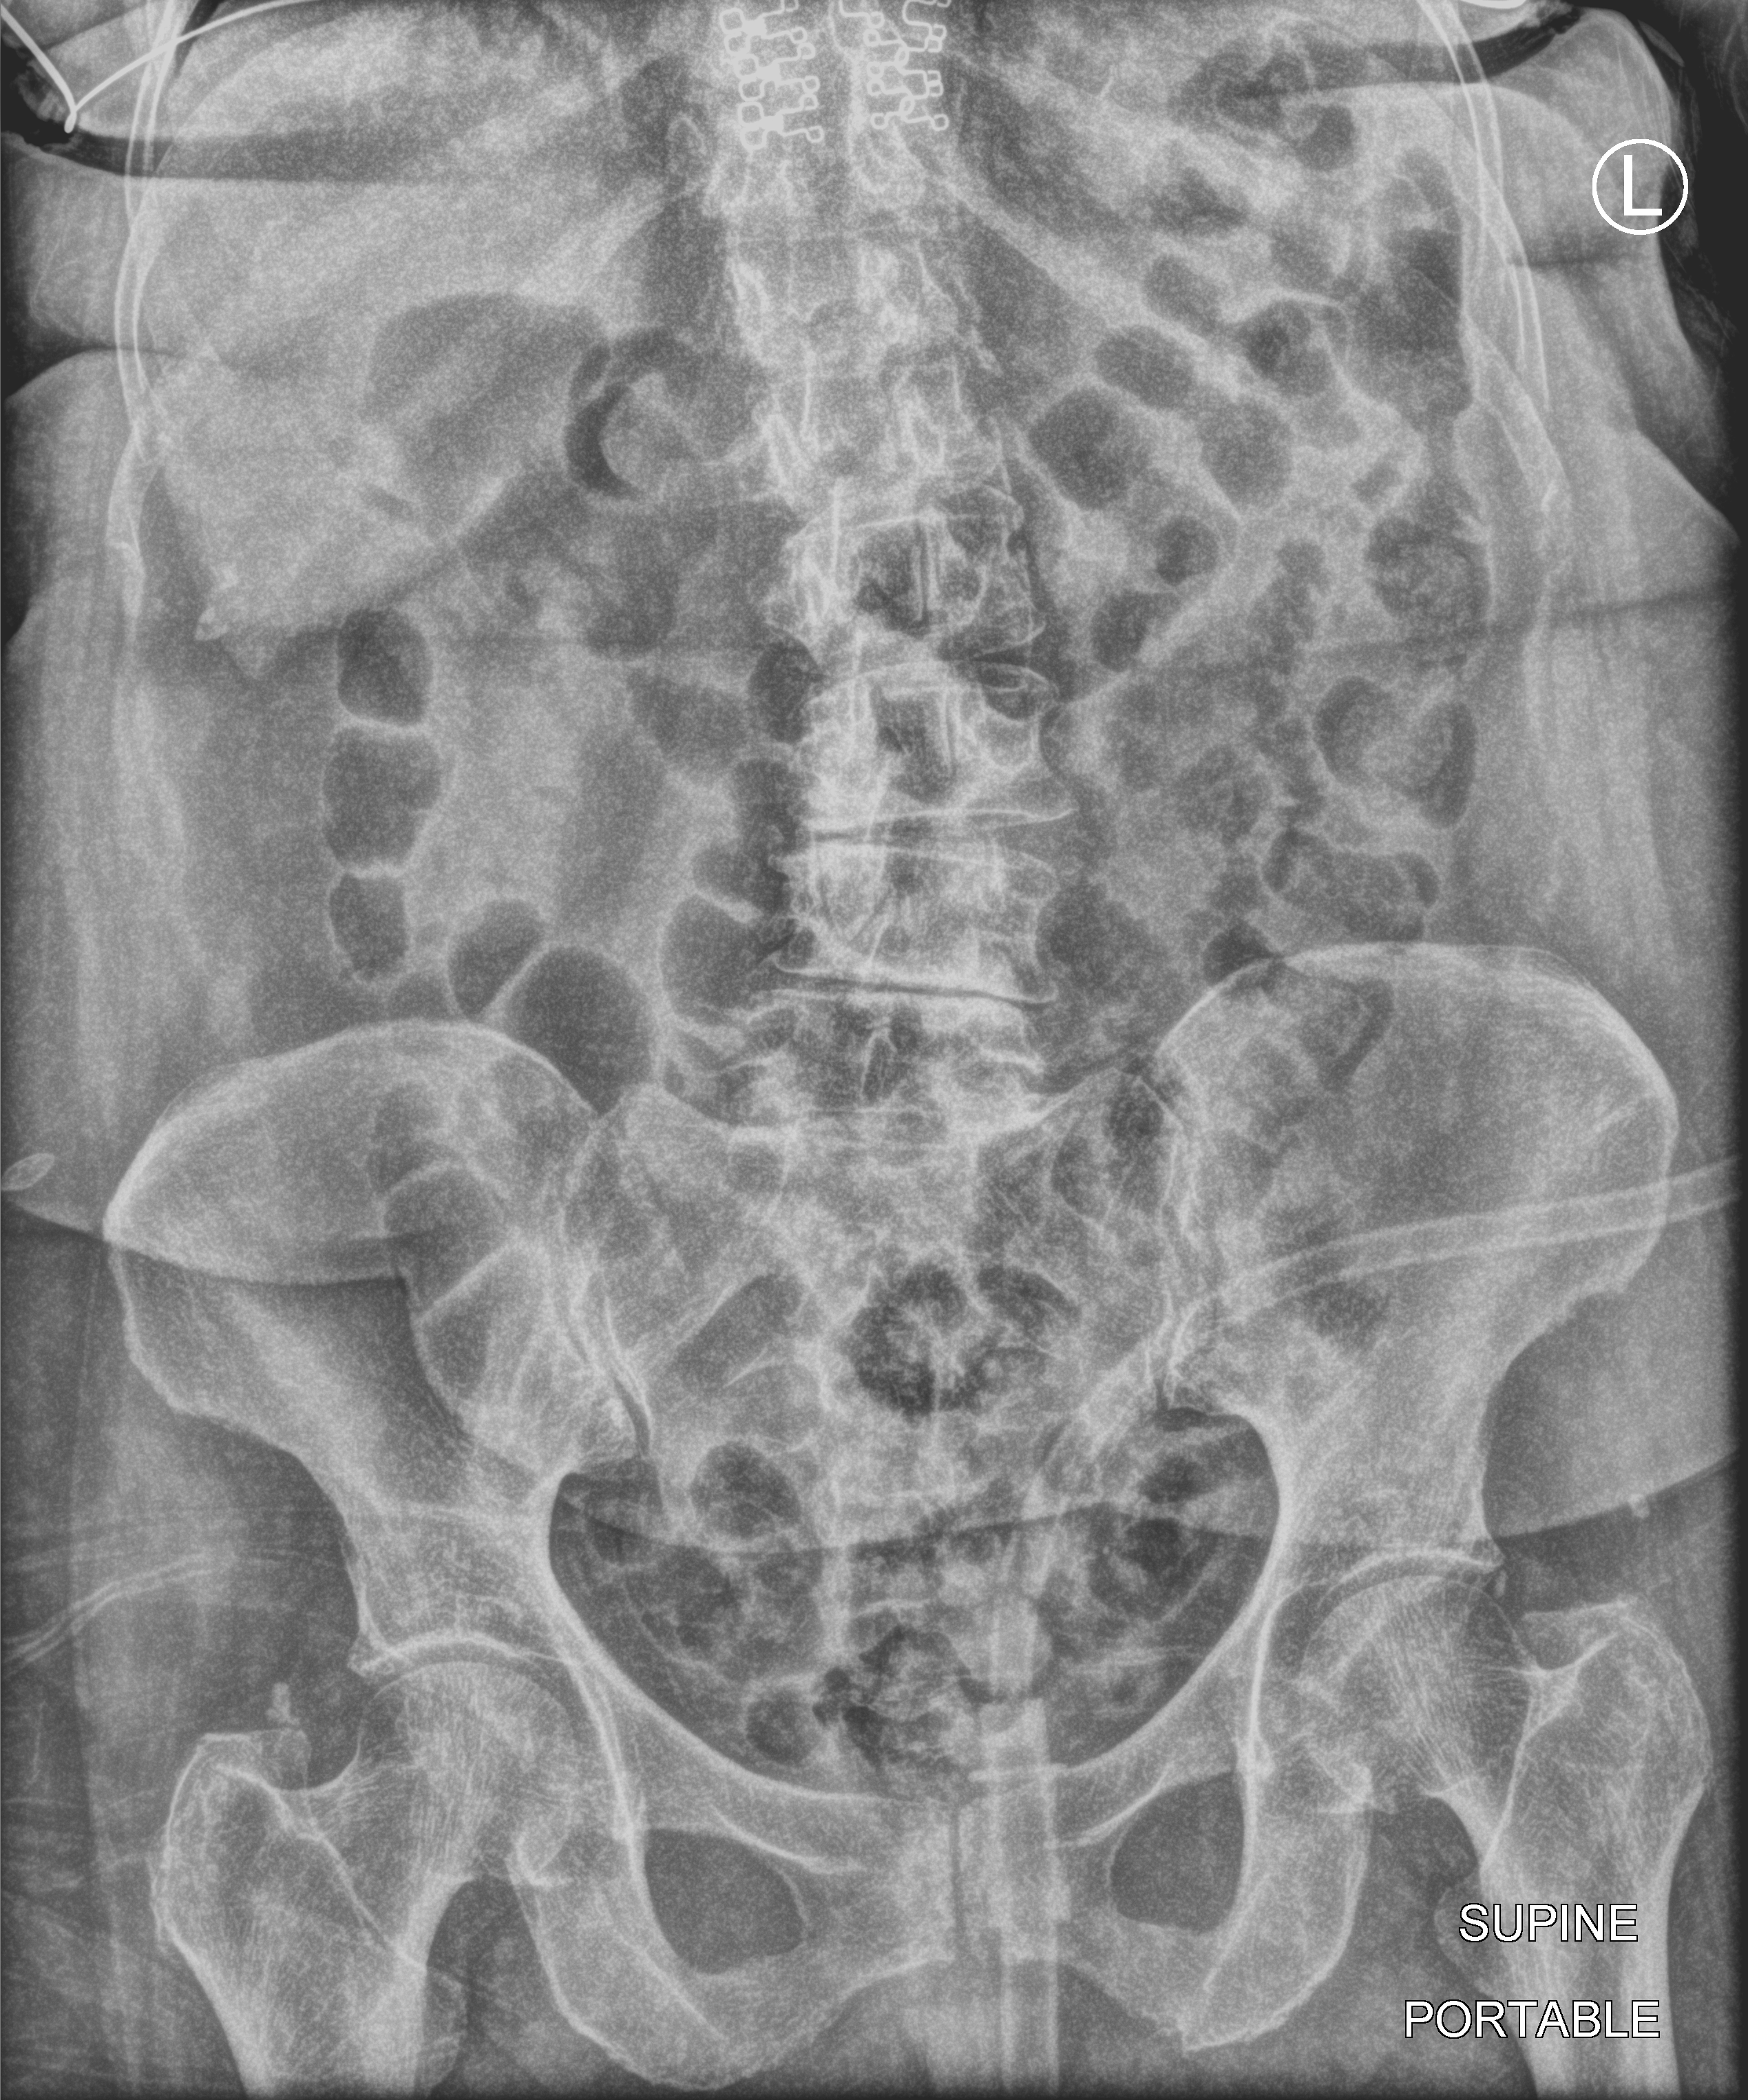
Abdomen X-ray (portable). Patient hospitalised with COVID-19; female, aged 75–90 years.
Hospital-stay facts (about this admission, not read from this image; timing relative to this image not recorded): length of hospital stay: 8 days; diabetes (admission record): no.